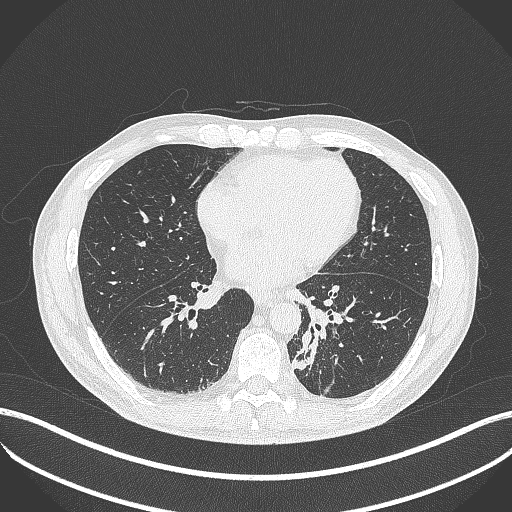
Chest CT, one axial slice. Position 163 of 451 along the scan axis. Reconstruction kernel B70f. 120 kVp. Lung window (W 1500 / L -600 HU). 1 mm slice thickness. 512 × 512 image matrix, field of view 400 × 400 mm. Patient: male, 72 years. Case-level facts recorded for this patient, not image findings: clinical TNM (as recorded): T2b N0 M1.
Structures marked on this image (rectangle marked by the reading radiologist):
- lung tumour (recorded histology: adenocarcinoma): bounding box <290,322,324,374> (left, top, right, bottom; pixels)